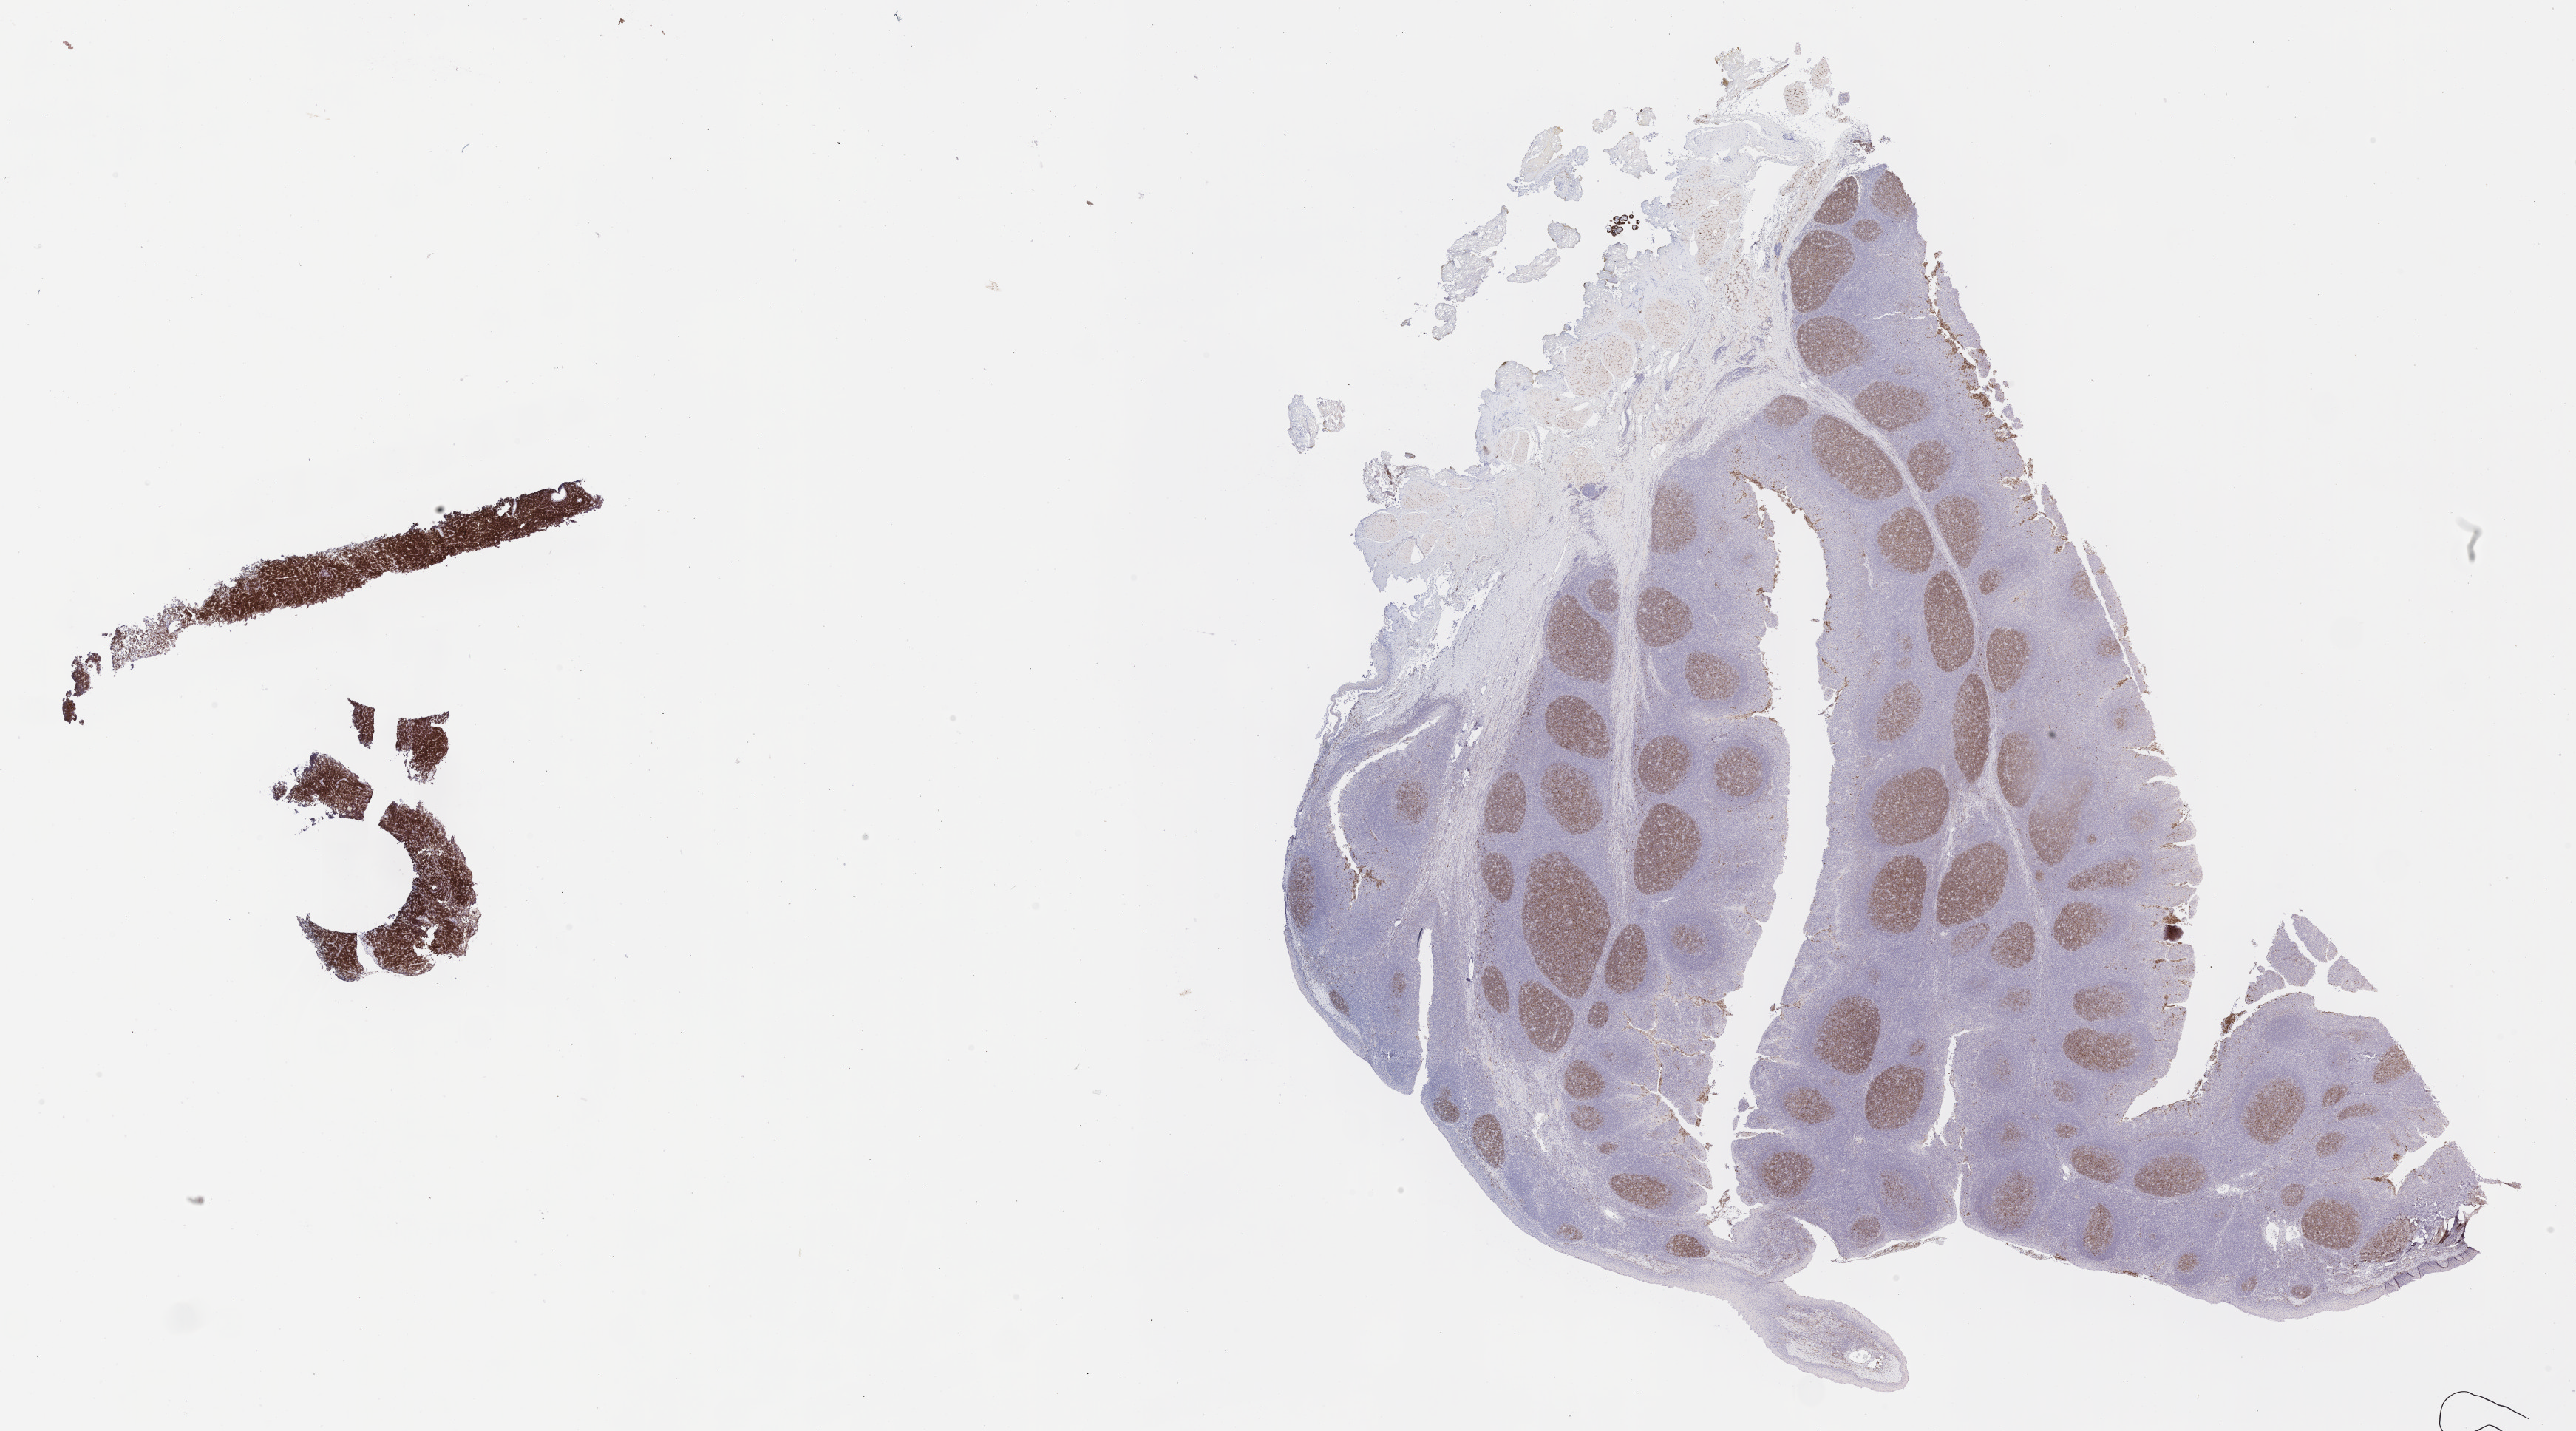
Whole-slide image, immunohistochemical stain for CD10 — low-resolution overview of the scanned area, about 28.2 x 15.7 mm, specimen: tumor tissue, site: ovary. Patient female; 10 years old.
* diagnosis: Burkitt lymphoma, NOS